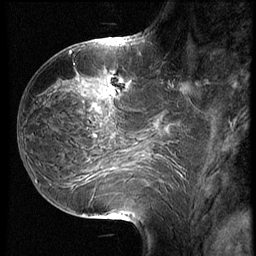
Breast MRI (dynamic contrast-enhanced), one sagittal slice; slice 27 of 68 in the series (ordered by position); 3 images stored at this slice position (order not interpretable as contrast timing); 1.5 T; TE 4.2 ms, TR 8.9 ms; 256 × 256 image matrix. Patient: female, 39 years. From the clinical record (not read from this slice): setting: breast cancer imaged before/during neoadjuvant chemotherapy; receptor status: HER2-positive.
Annotated regions visible in this slice (semi-automatic segmentation, software-assisted and operator-edited):
- analysis volume of interest (the breast-tissue region the enhancement analysis was run in; not a lesion): bounding box (x1, y1, x2, y2) in pixels: (66, 68, 141, 127)
- tumour enhancement mask (voxels above the 140 % enhancement threshold inside the analysis volume of interest): (108, 88, 113, 93)